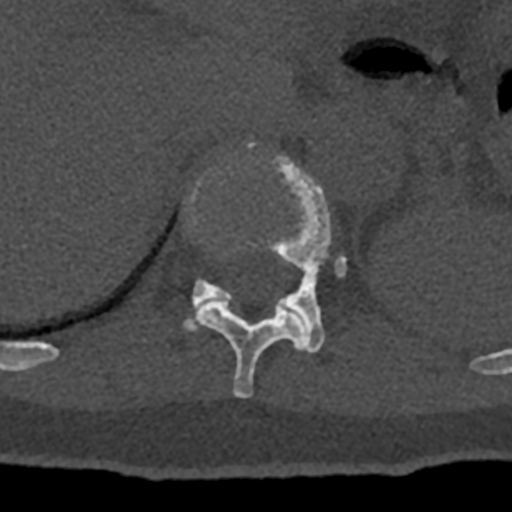
CT including the spine, one axial slice. Slice 524 of 797 in the series (ordered by position). 120 kVp. Bone window (W 1800 / L 400 HU). 0.5 mm slice thickness. 512 × 512 image matrix, field of view 160 × 160 mm. Male patient, age 74 years. Case-level facts recorded for this patient, not image findings: primary cancer: renal.
Annotated regions visible in this slice (semi-automatically segmented with operator editing):
- T11 vertebra: box from (x=194, y=241) to (x=307, y=398) px
- T12 vertebra: (x=183, y=144)–(x=347, y=354)